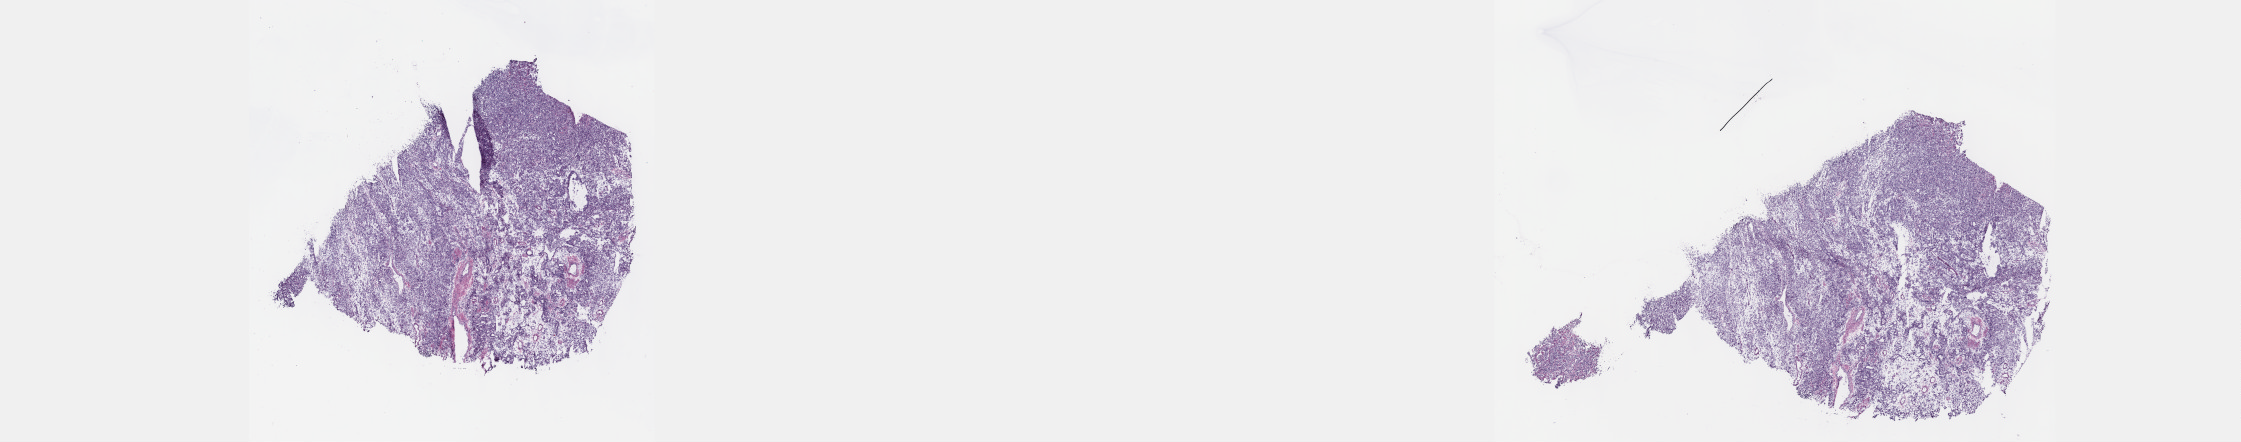
Whole-slide histology image, Hematoxylin and eosin (H&E) stained, low-resolution overview of the scanned area, about 36.2 x 7.1 mm (from a 40x scan); frozen section from the top of the tissue portion; sample: primary tumour, esophagus. Patient: male, age at initial diagnosis 43 years. Histologic grade: G3 (poorly differentiated). Composition of this section per pathologist review: tumour cells 80%, tumour nuclei 80%, normal cells 0%, stromal cells 20%, necrosis 0%. Inflammatory infiltration, as recorded: lymphocyte infiltration 40%, monocyte infiltration 20%, neutrophil infiltration 20%.
• TNM: T3 N1 M0
• AJCC pathologic stage: III (5th edition)
• diagnosis: Adenocarcinoma, NOS (lower third of esophagus)